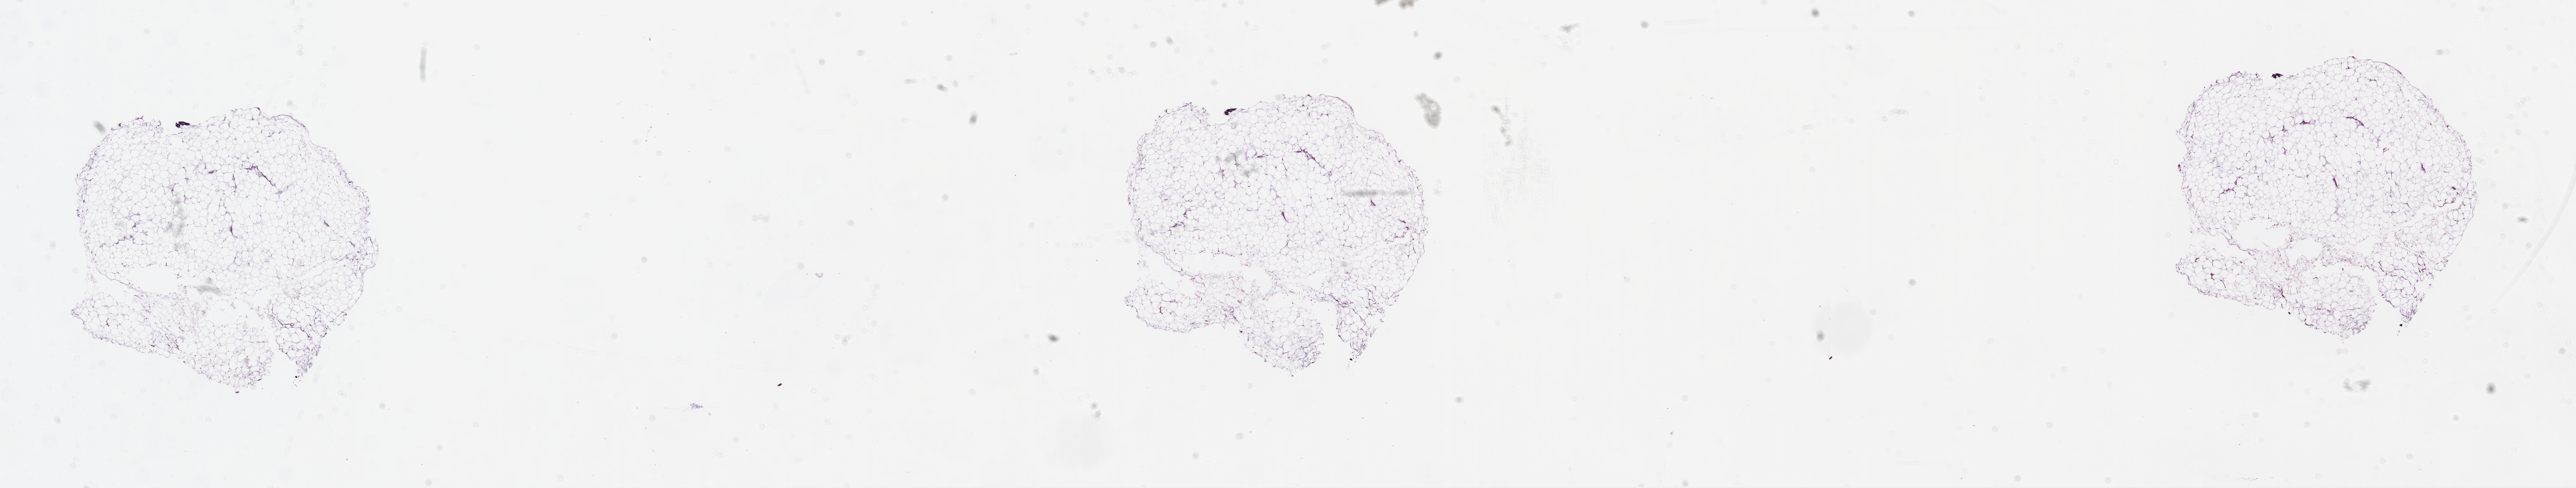
Digitized H&E-stained tissue section (whole slide) — whole scanned area (about 31.1 x 5.9 mm) shown as a low-resolution overview. Frozen section from the top of the tissue portion. Primary tumour sample from the colon. Male, age 78 years at initial diagnosis. Slide review estimates, as recorded: tumour cells 0%, tumour nuclei 0%, normal cells 100%, stromal cells 0%, necrosis 0%.
Lymph nodes positive (case pathology): 0 of 11 examined. AJCC pathologic stage: IIA. Histologic diagnosis: Adenocarcinoma, NOS (sigmoid colon).